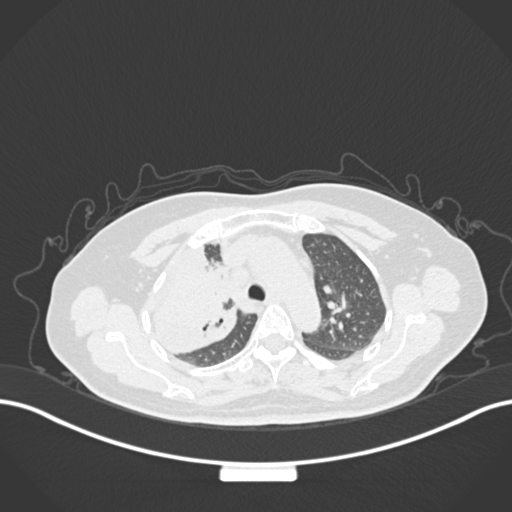
Chest CT, one axial slice; position 115 of 177 along the scan axis; 120 kVp; lung window (W 1500 / L -600 HU); 1 mm slice thickness; 512 × 512 image matrix, field of view 400 × 400 mm. Patient: female, 60 years. From the clinical record (not read from this slice): clinical TNM (as recorded): T3 N1 M1.
Structures marked on this image (rectangle marked by the reading radiologist):
- lung tumour (recorded histology: adenocarcinoma): box from (x=142, y=237) to (x=242, y=354) px